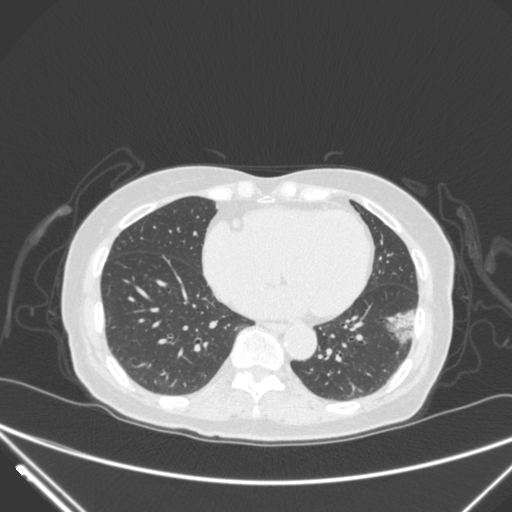
Chest CT, one axial slice; slice 111 of 310 in the series (ordered by position); 120 kVp; lung window (W 1500 / L -600 HU); 512 × 512 image matrix. Patient: female, 82 years. Case-level facts recorded for this patient, not image findings: clinical TNM (as recorded): T1c N0 M0.
Annotated regions visible in this slice (bounding box drawn by a radiologist):
- lung tumour (recorded histology: adenocarcinoma): bounding box <384,299,428,352> (left, top, right, bottom; pixels)